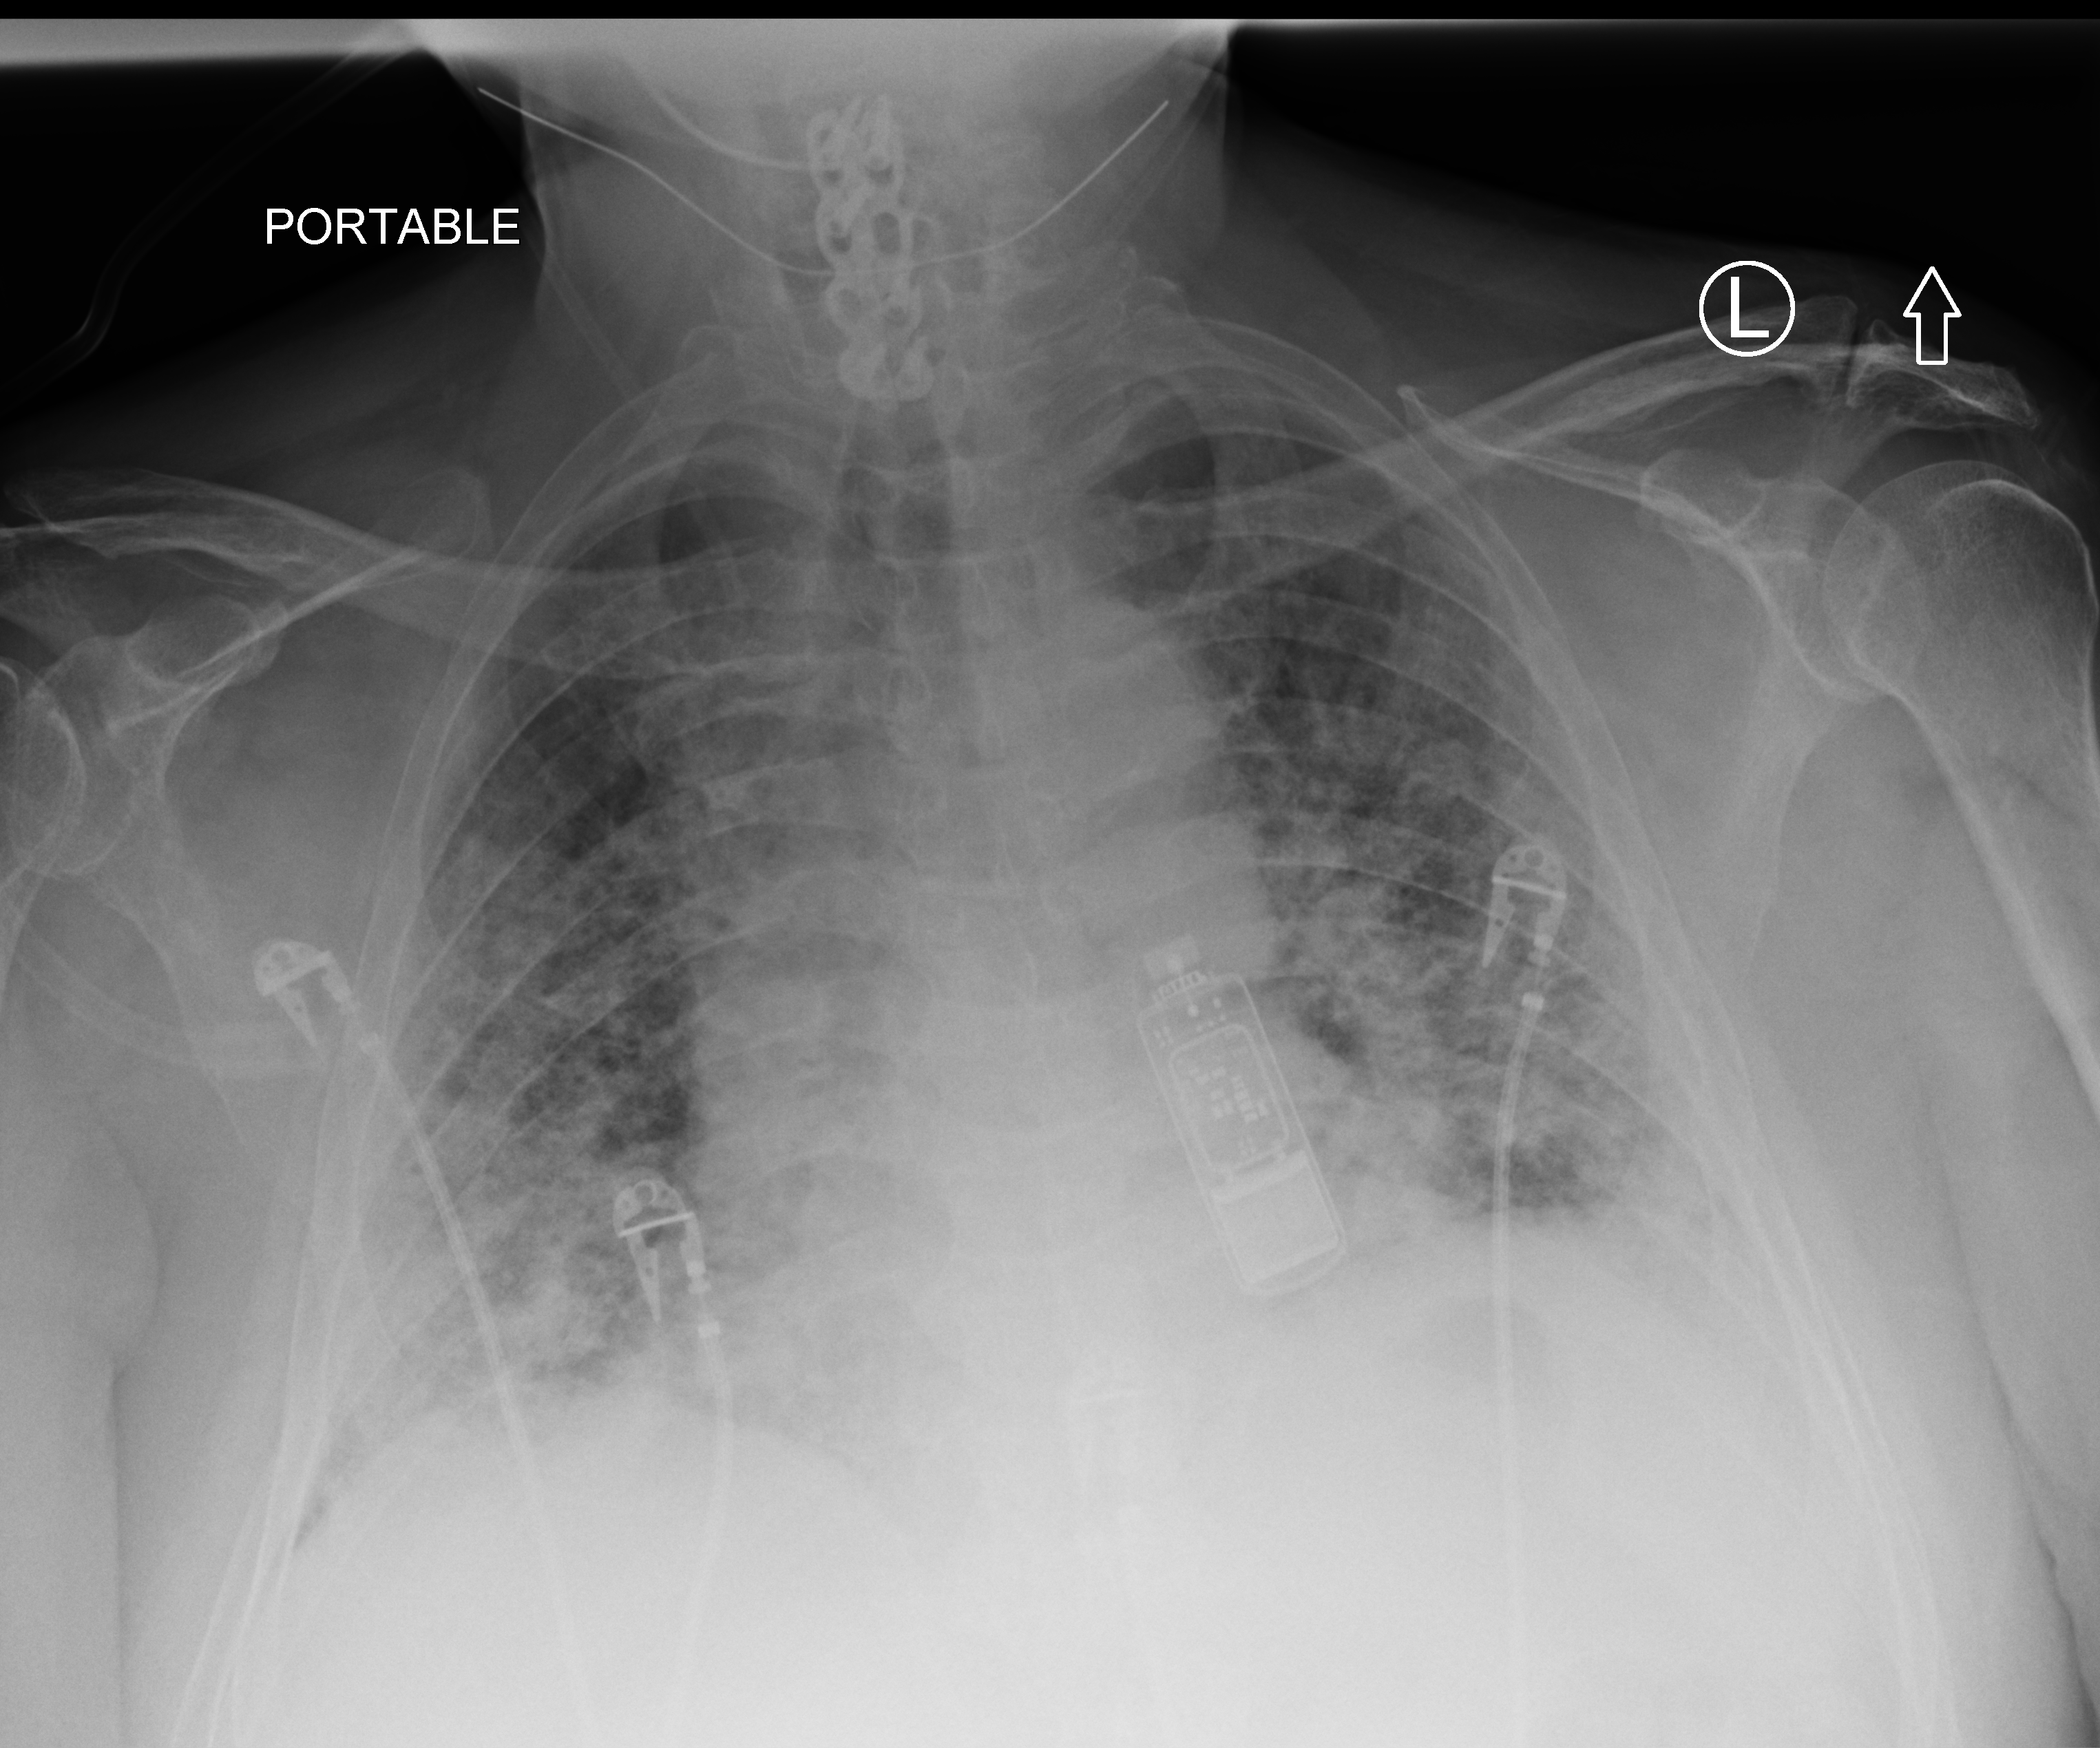
Bedside chest radiograph (computed radiography); anteroposterior (AP) projection. Male patient hospitalised with COVID-19, age 60–74 years.
Hospital-stay facts (about this admission, not read from this image; timing relative to this image not recorded): mechanically ventilated during this hospital stay: yes.